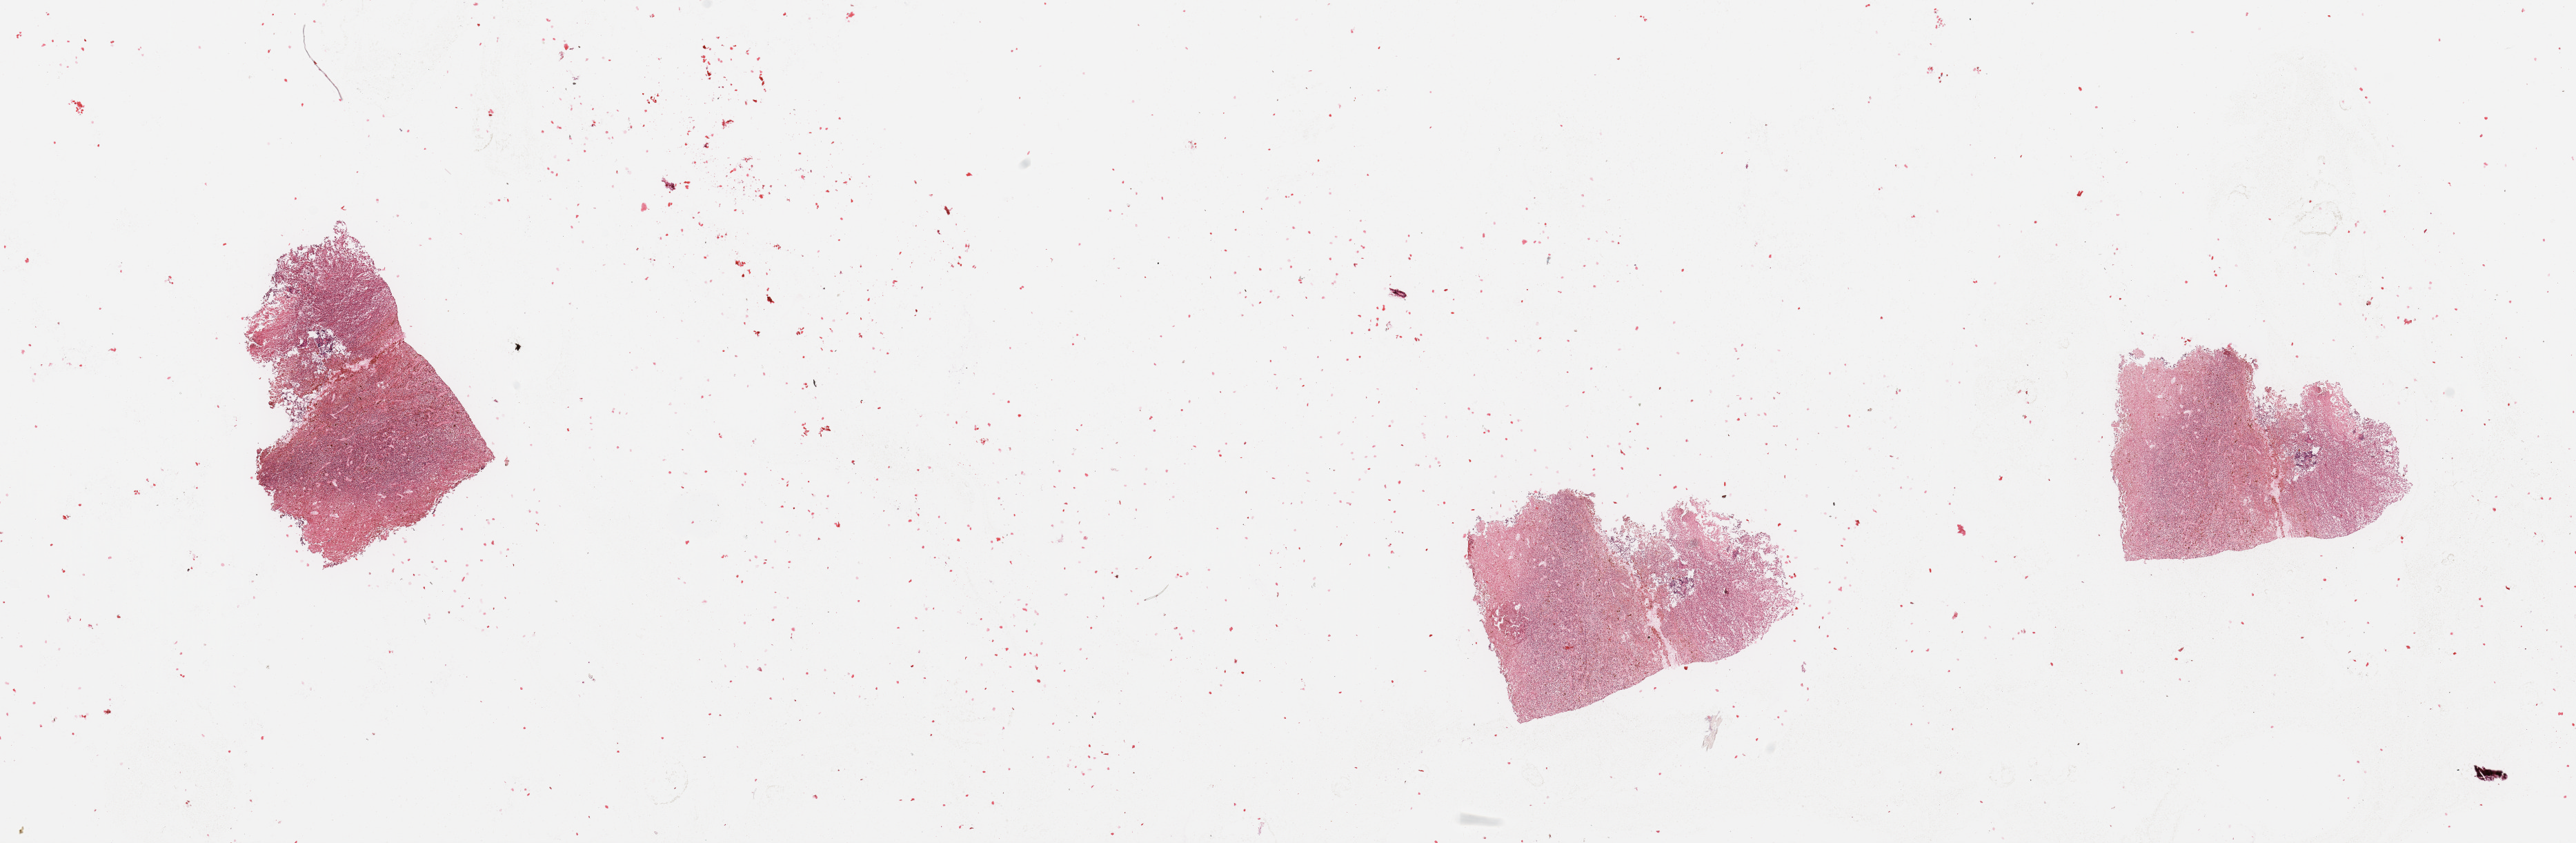
Digitized H&E tissue section (whole slide), low-resolution overview of the scanned area, about 29.5 x 9.7 mm. Tumour tissue sample, sampled site: lymph node. 76-year-old male patient. Slide review estimates, as recorded: tumour nuclei 90%, necrosis 10%.
- this section: metastatic tumour tissue
- patient diagnosis: Malignant melanoma, NOS